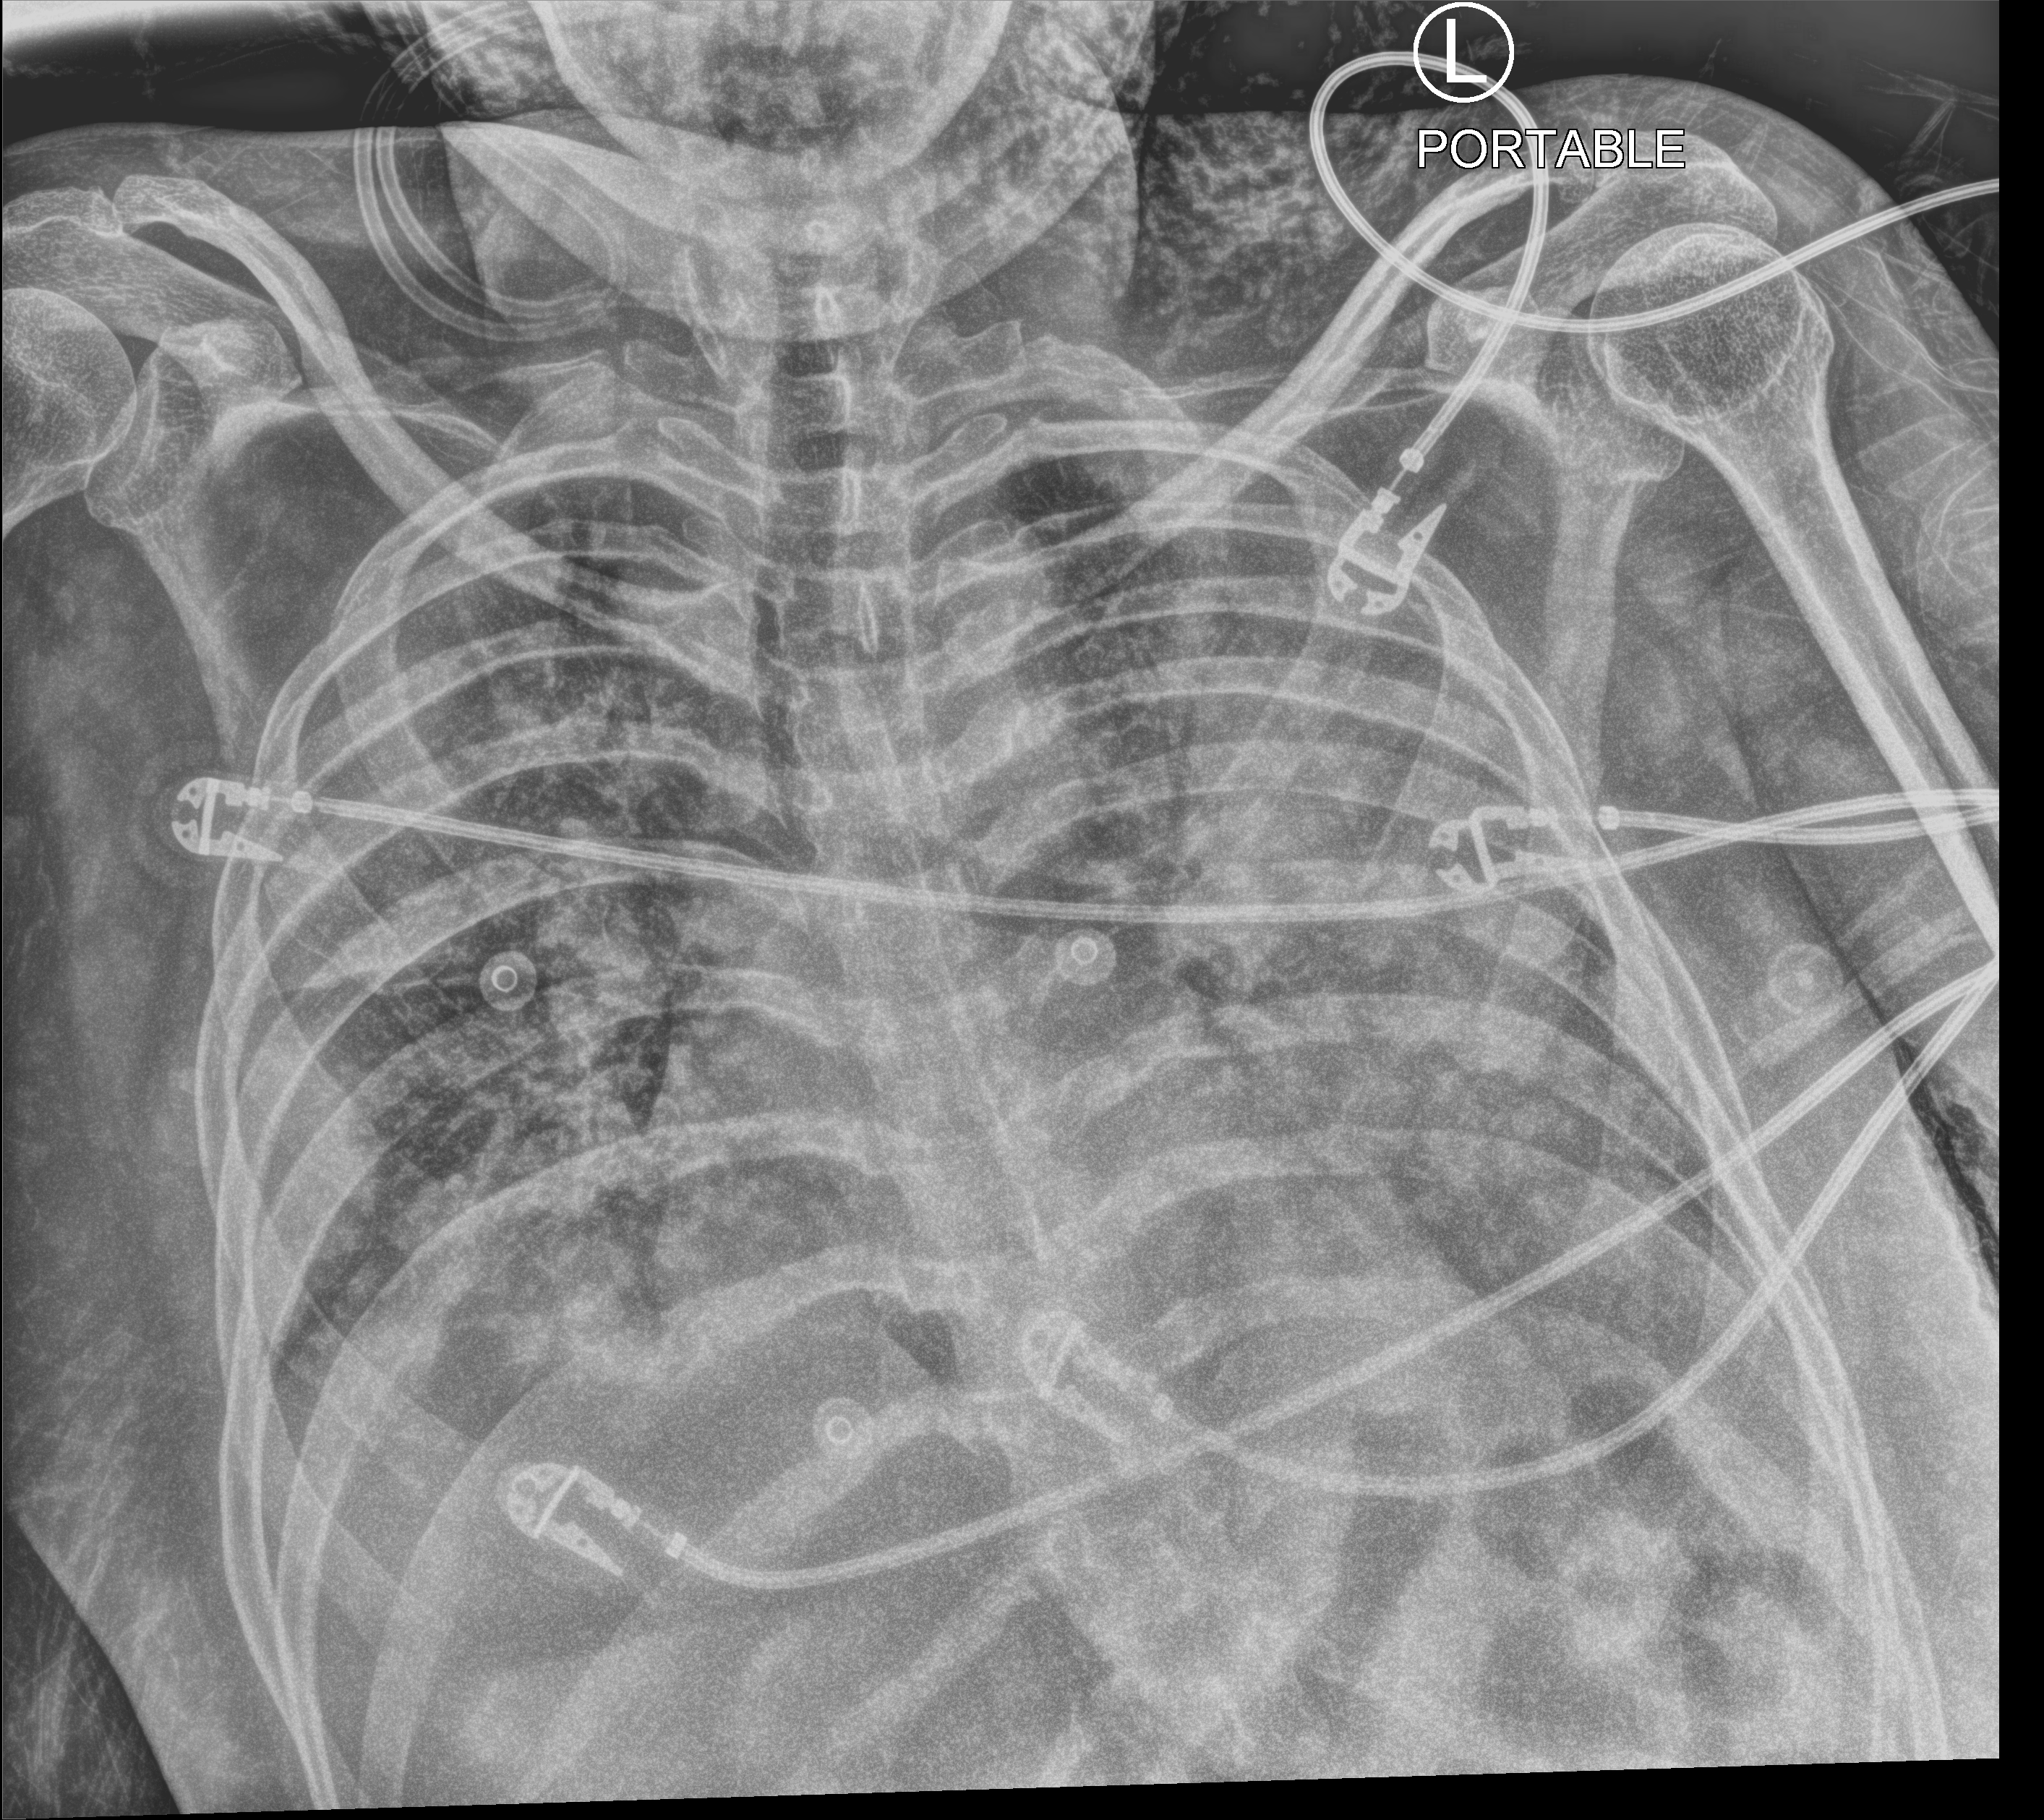
Chest X-ray (portable); anteroposterior (AP) projection. Patient hospitalised with COVID-19, aged 18–59 years.
Admission-level facts for this patient (not findings on this image; timing relative to this image not recorded): mechanically ventilated during this hospital stay: yes.